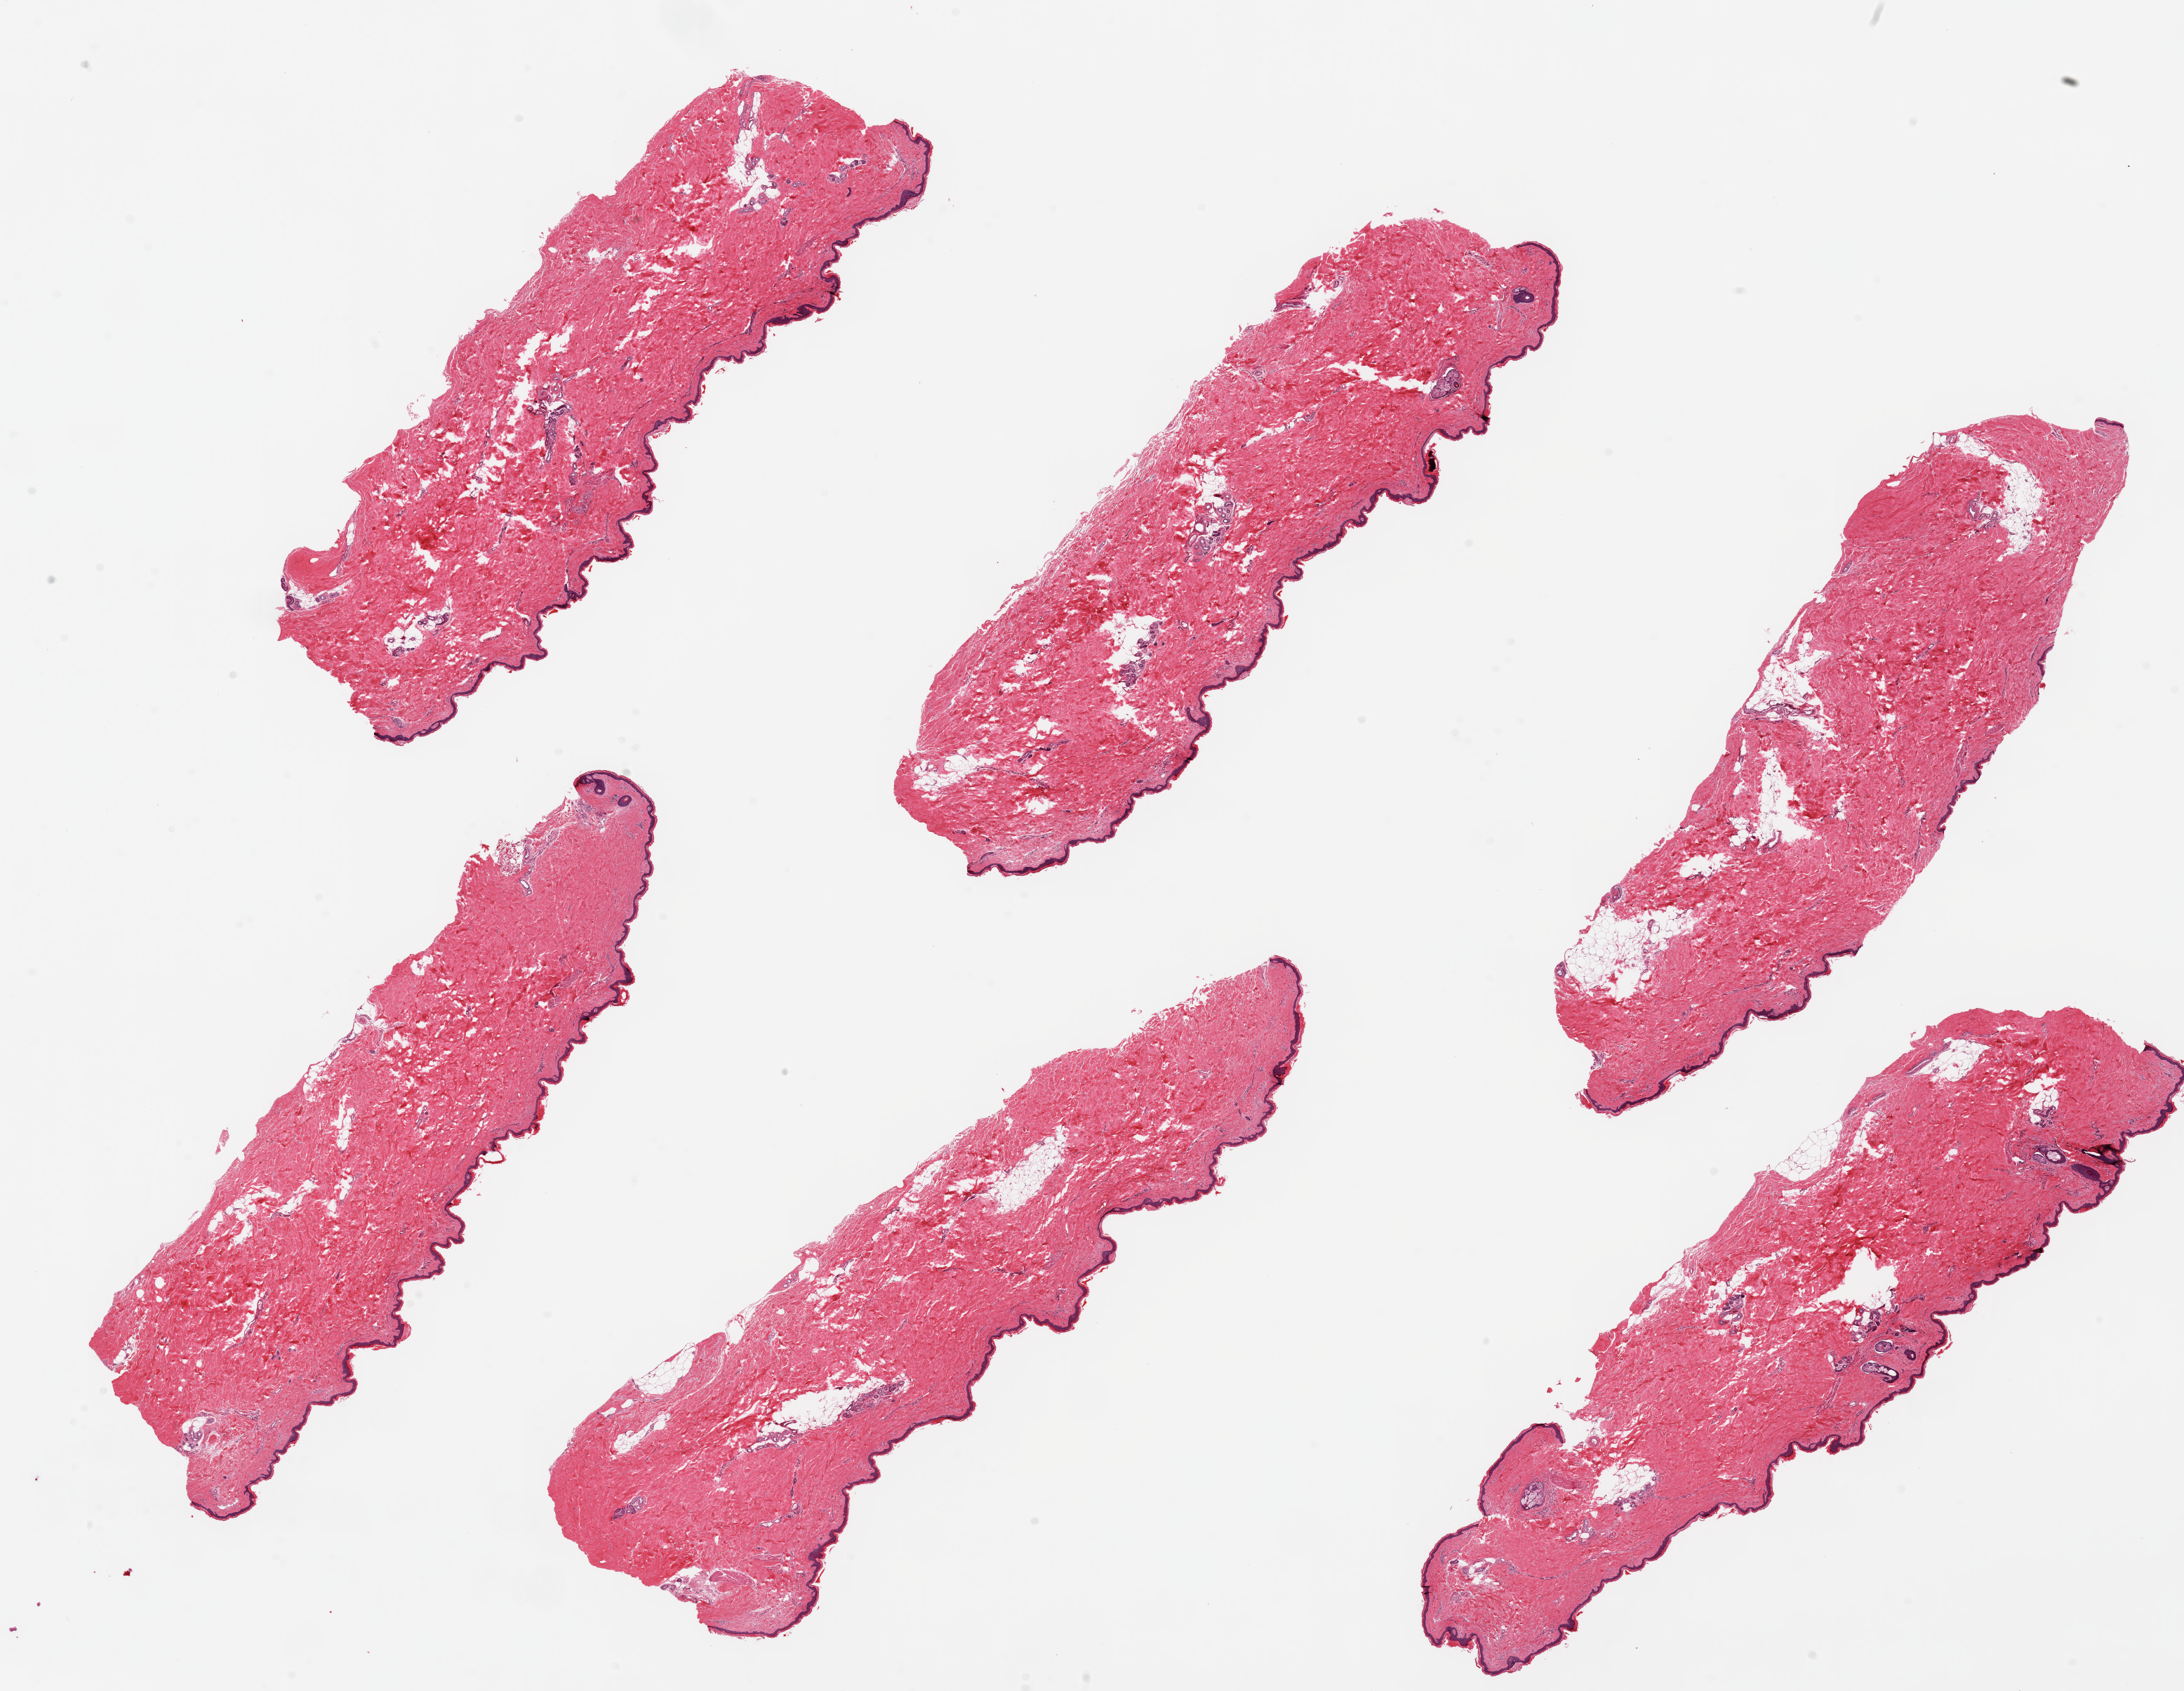
Hematoxylin and eosin (H&E) whole-slide image — a low-resolution overview of the entire scanned area, about 24.6 x 19.1 mm; PAXgene-fixed paraffin-embedded (PFPE) section; section of skin of lower leg (target tissue); donor tissue sample. Male donor.
Review note (as recorded): 6 pieces up to 10x3 mm; well trimmed of subcutaneous adipose.